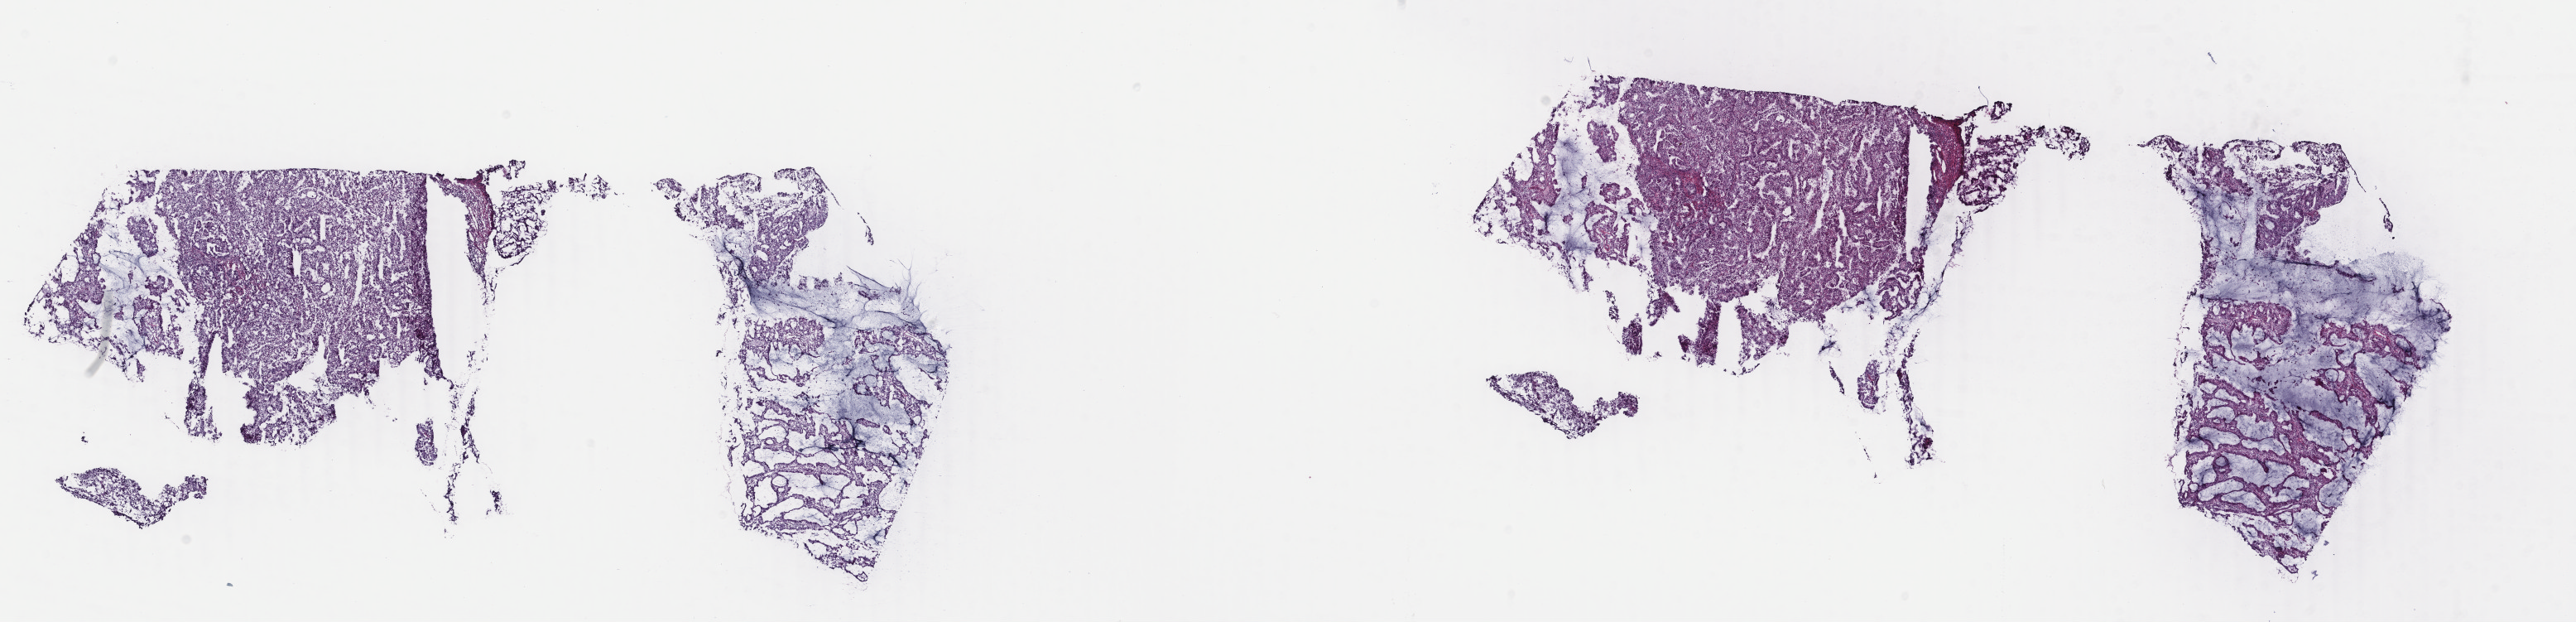
Digitized Hematoxylin and eosin (H&E) stained tissue section (whole slide) — a low-resolution overview of the entire scanned area, about 24.7 x 6.0 mm (slide scanned at 40x). Frozen section. Uterus, primary tumour sample. Female, age 59 years at initial diagnosis. Histologic grade: G1 (well differentiated). Composition of this section per pathologist review: tumour cells 100%, tumour nuclei 75%, normal cells 0%, stromal cells 0%, necrosis 0%. Inflammatory infiltration, as recorded: lymphocyte infiltration 0%, monocyte infiltration 0%, neutrophil infiltration 0%.
- FIGO stage: IB
- histologic diagnosis: Endometrioid adenocarcinoma, secretory variant (endometrium)